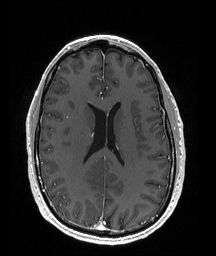
Brain MRI from a brain-tumour surgery series, one axial slice. Position 76 of 176 along the scan axis. T1-weighted post-contrast. 1 mm slice thickness. 216 × 256 image matrix. Case-level facts recorded for this patient, not image findings: histopathology: Oligodendroglioma; WHO grade: 2; IDH mutation: yes.
Annotated regions visible in this slice (manually delineated by an expert):
- tumour: bounding box (x1, y1, x2, y2) in pixels: (71, 168, 88, 194)